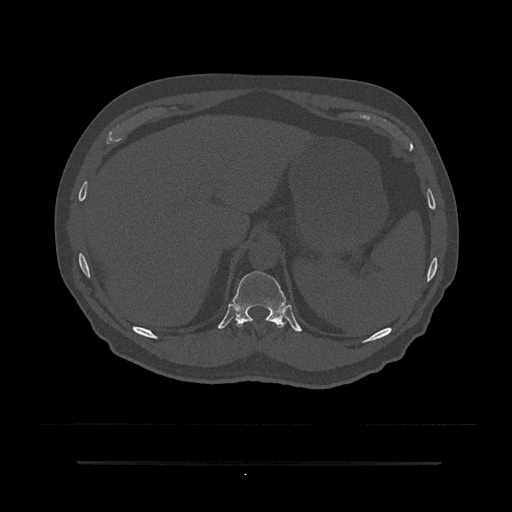
CT including the spine, one axial slice; position 286 of 797 along the scan axis; bone window (W 1800 / L 400 HU); 0.5 mm slice thickness; 512 × 512 image matrix. Patient: male, 59 years. Case-level facts recorded for this patient, not image findings: primary cancer: bile ducts; vertebrae with lytic lesions (as recorded): T10.
Annotated regions visible in this slice (semi-automatic segmentation, software-assisted and operator-edited):
- T11 vertebra: box from (x=231, y=271) to (x=290, y=328) px